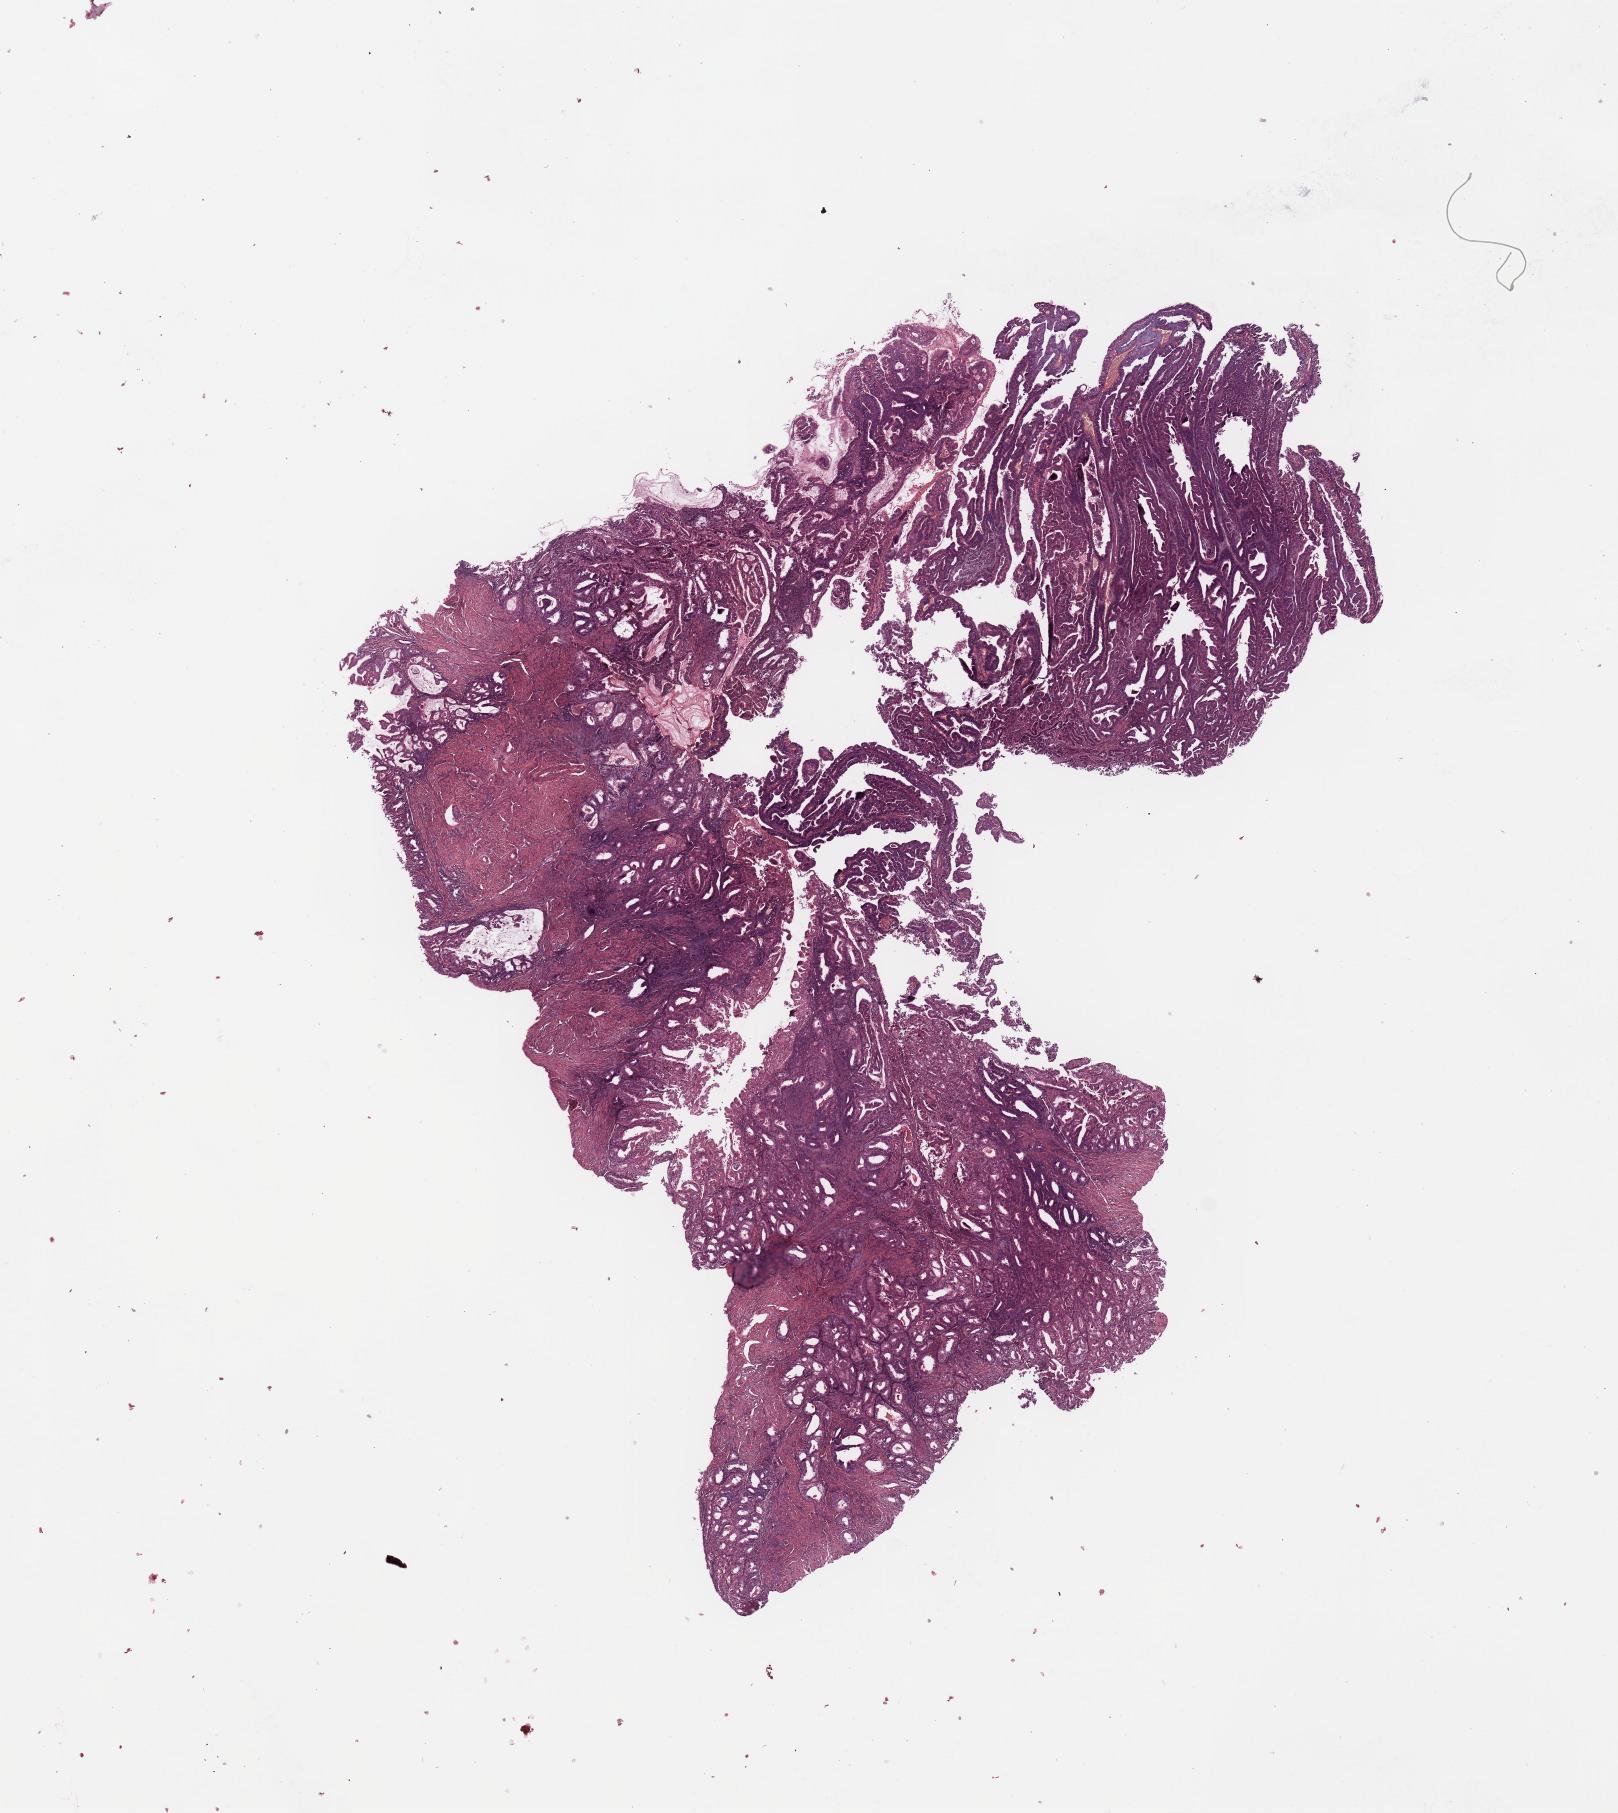
Whole-slide histology image, Hematoxylin and eosin (H&E) stained, shown as a low-resolution overview of the whole scanned area (about 12.8 x 14.3 mm, from a 20x scan); tumour tissue sample, sampled site: uterus. 57-year-old female patient. Histologic grade: G1 (well differentiated). Slide review estimates, as recorded: tumour nuclei 90%, necrosis 0%.
Histologic diagnosis: Endometrioid adenocarcinoma, NOS. AJCC pathologic stage: I.